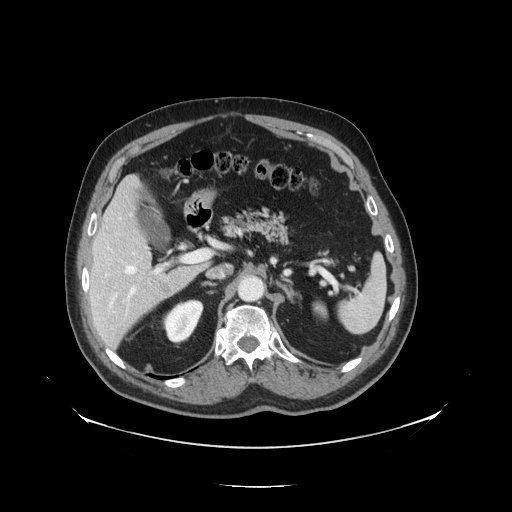
Contrast-enhanced abdominal CT, one axial slice; position 82 of 138 along the scan axis; reconstruction kernel STANDARD; 120 kVp; intravenous contrast given; soft-tissue window (W 400 / L 40 HU); 2.5 mm slice thickness; 512 × 512 image matrix. Male patient, age 77 years. Case-level facts recorded for this patient, not image findings: diagnosis: colorectal cancer liver metastases, imaged before liver resection; multiple liver metastases: no; largest metastasis: 1.5 cm; disease in both lobes: no.
Outlined on this slice (outlined manually by an expert reader):
- hepatic veins: box from (x=125, y=265) to (x=136, y=274) px
- liver: (x=90, y=179)–(x=208, y=348)
- planned liver remnant (the part of the liver to remain after resection): (x=90, y=178)–(x=156, y=288)
- portal vein (with intrahepatic branches): (x=125, y=253)–(x=205, y=305)
- liver metastasis: (x=158, y=281)–(x=171, y=293)